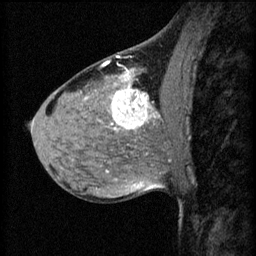
Breast MRI (dynamic contrast-enhanced), one sagittal slice; slice 32 of 60 in the series (ordered by position); 3 images stored at this slice position (order not interpretable as contrast timing); 1.5 T; TE 4.2 ms, TR 8.2 ms; 256 × 256 image matrix, field of view 180 × 180 mm. Patient: female, 40 years.
Annotated regions visible in this slice (semi-automatically segmented with operator editing):
- analysis volume of interest (the breast-tissue region the enhancement analysis was run in; not a lesion): box from (x=108, y=82) to (x=175, y=139) px
- tumour enhancement mask (voxels above the 70 % enhancement threshold inside the analysis volume of interest): (x=112, y=84)–(x=161, y=131)